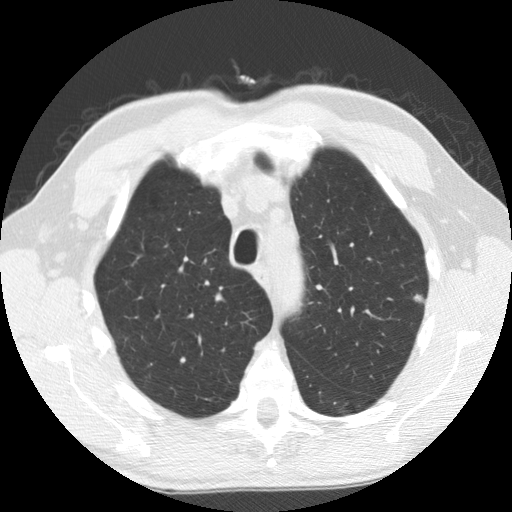
Axial slice from a low-dose chest CT screening exam, third annual screen, lung window (W 1500 / L -600 HU), 2.5 mm slice thickness, standard (soft-tissue) reconstruction kernel (STANDARD), slice 30 of 158 in the series. Male, age 63 years at enrolment. Current smoker at enrolment.
Lesion marked by an expert reader, bounding box <401,281,440,314> (left, top, right, bottom; pixels). Screening reader's record for this exam (one nodule recorded; not confirmed to be the boxed lesion): non-calcified nodule or mass ≥4 mm, left upper lobe, 8 × 6 mm, smooth margins, ground glass attenuation, pre-existing on the prior screen: yes; interval growth: yes. Official screen result: positive, other. Later outcome: lung cancer diagnosed 52 days after this screen — adenocarcinoma, NOS, left upper lobe, well differentiated (G1), stage IB (AJCC 6th edition), 5 mm at pathology.